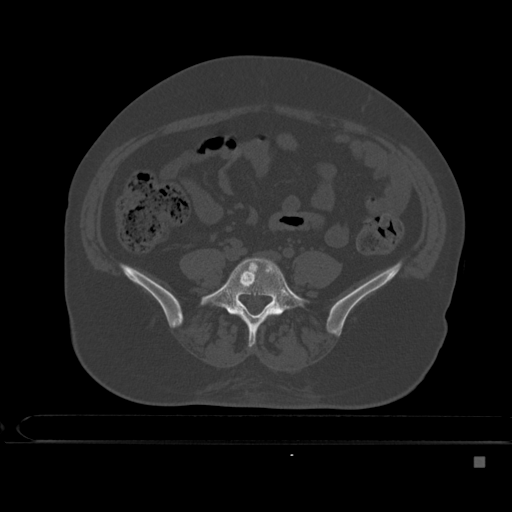
CT including the spine, one axial slice; slice 111 of 495 in the series (ordered by position); bone window (W 1800 / L 400 HU); 1.5 mm slice thickness; 512 × 512 image matrix. Patient: female, 33 years. Case-level facts recorded for this patient, not image findings: primary cancer: breast; vertebrae with lytic lesions (as recorded): T1.
Structures marked on this image (semi-automatic segmentation, software-assisted and operator-edited):
- L5 vertebra: bounding box [x1, y1, x2, y2] px = [200, 257, 310, 347]